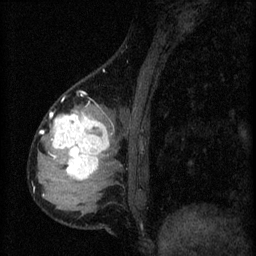
Breast MRI (dynamic contrast-enhanced), one sagittal slice; slice 17 of 60 in the series (ordered by position); 3 images stored at this slice position (order not interpretable as contrast timing); 1.5 T; TE 4.2 ms, TR 8.2 ms; 2 mm slice thickness; 256 × 256 image matrix, field of view 180 × 180 mm. Female patient, age 37 years.
Annotated regions visible in this slice (semi-automatic segmentation, software-assisted and operator-edited):
- analysis volume of interest (the breast-tissue region the enhancement analysis was run in; not a lesion): bounding box <44,104,119,197> (left, top, right, bottom; pixels)
- tumour enhancement mask (voxels above the 70 % enhancement threshold inside the analysis volume of interest): <52,112,111,181>